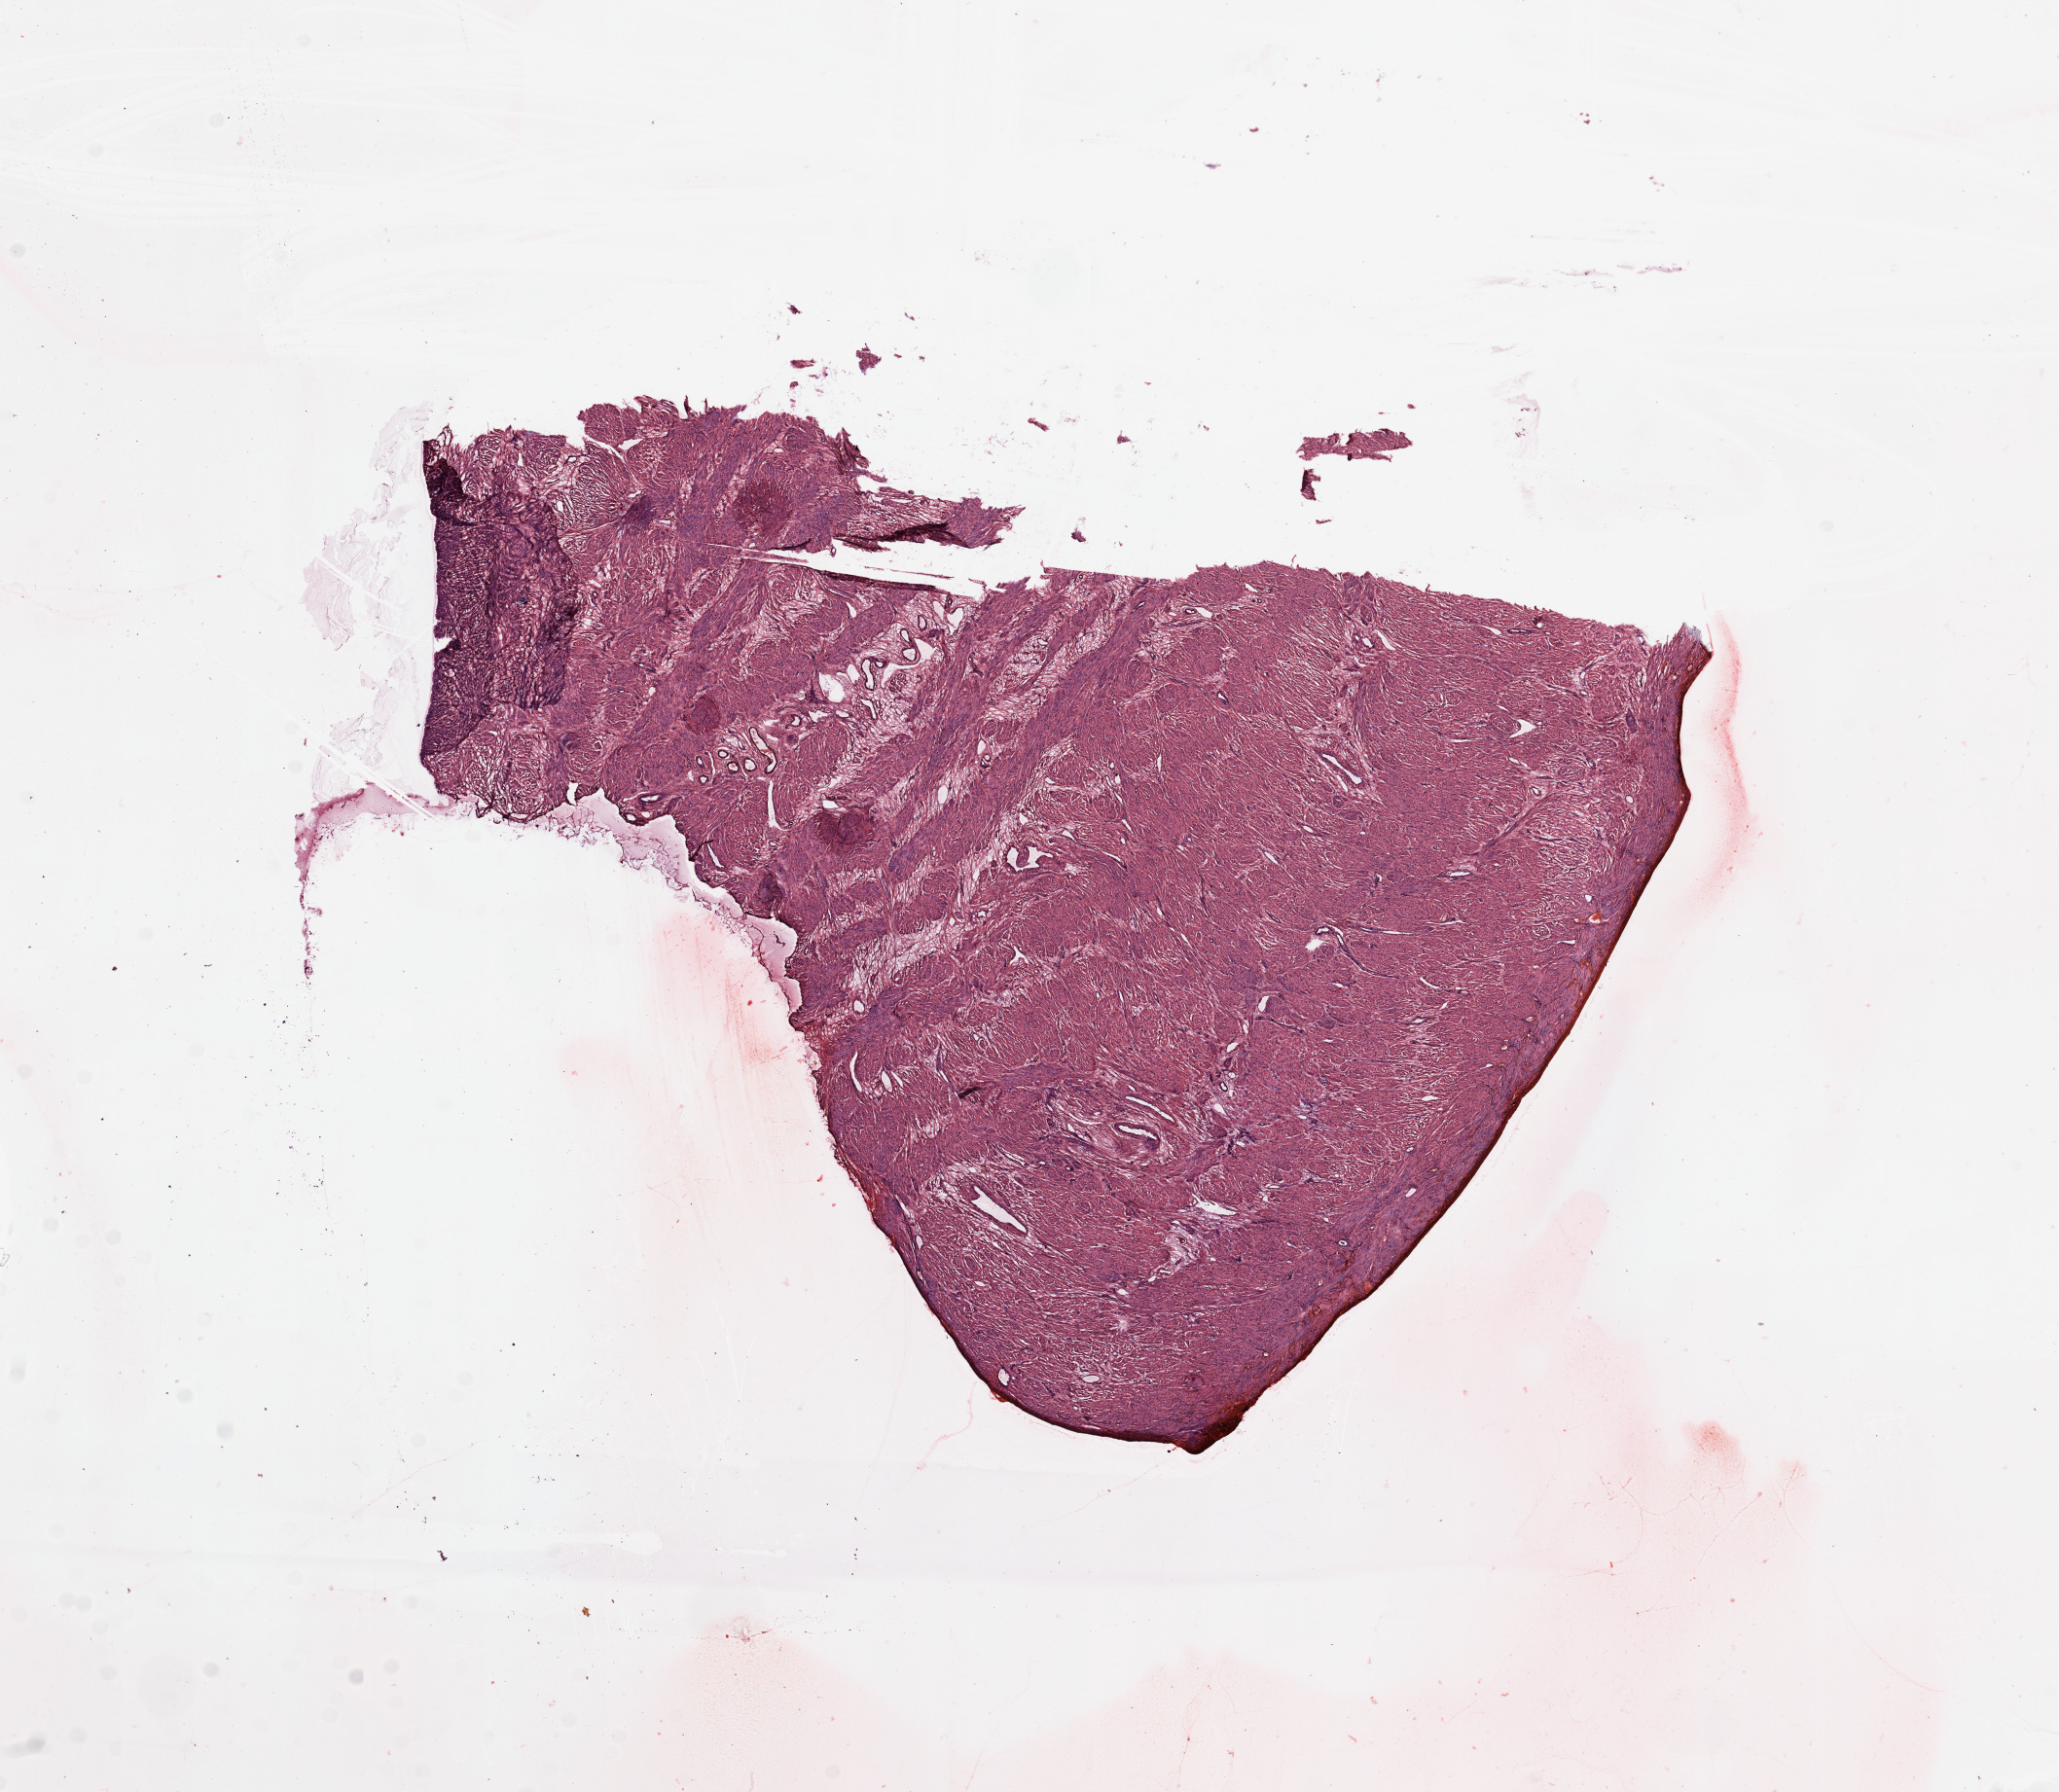
Hematoxylin and eosin (H&E) stained whole-slide image — whole scanned area (about 16.7 x 14.6 mm) shown as a low-resolution overview. Uterus, normal (non-tumour) tissue. Female, 45 y/o.
This section: normal (non-tumour) tissue from the same patient. Patient diagnosis: Endometrioid adenocarcinoma, NOS.